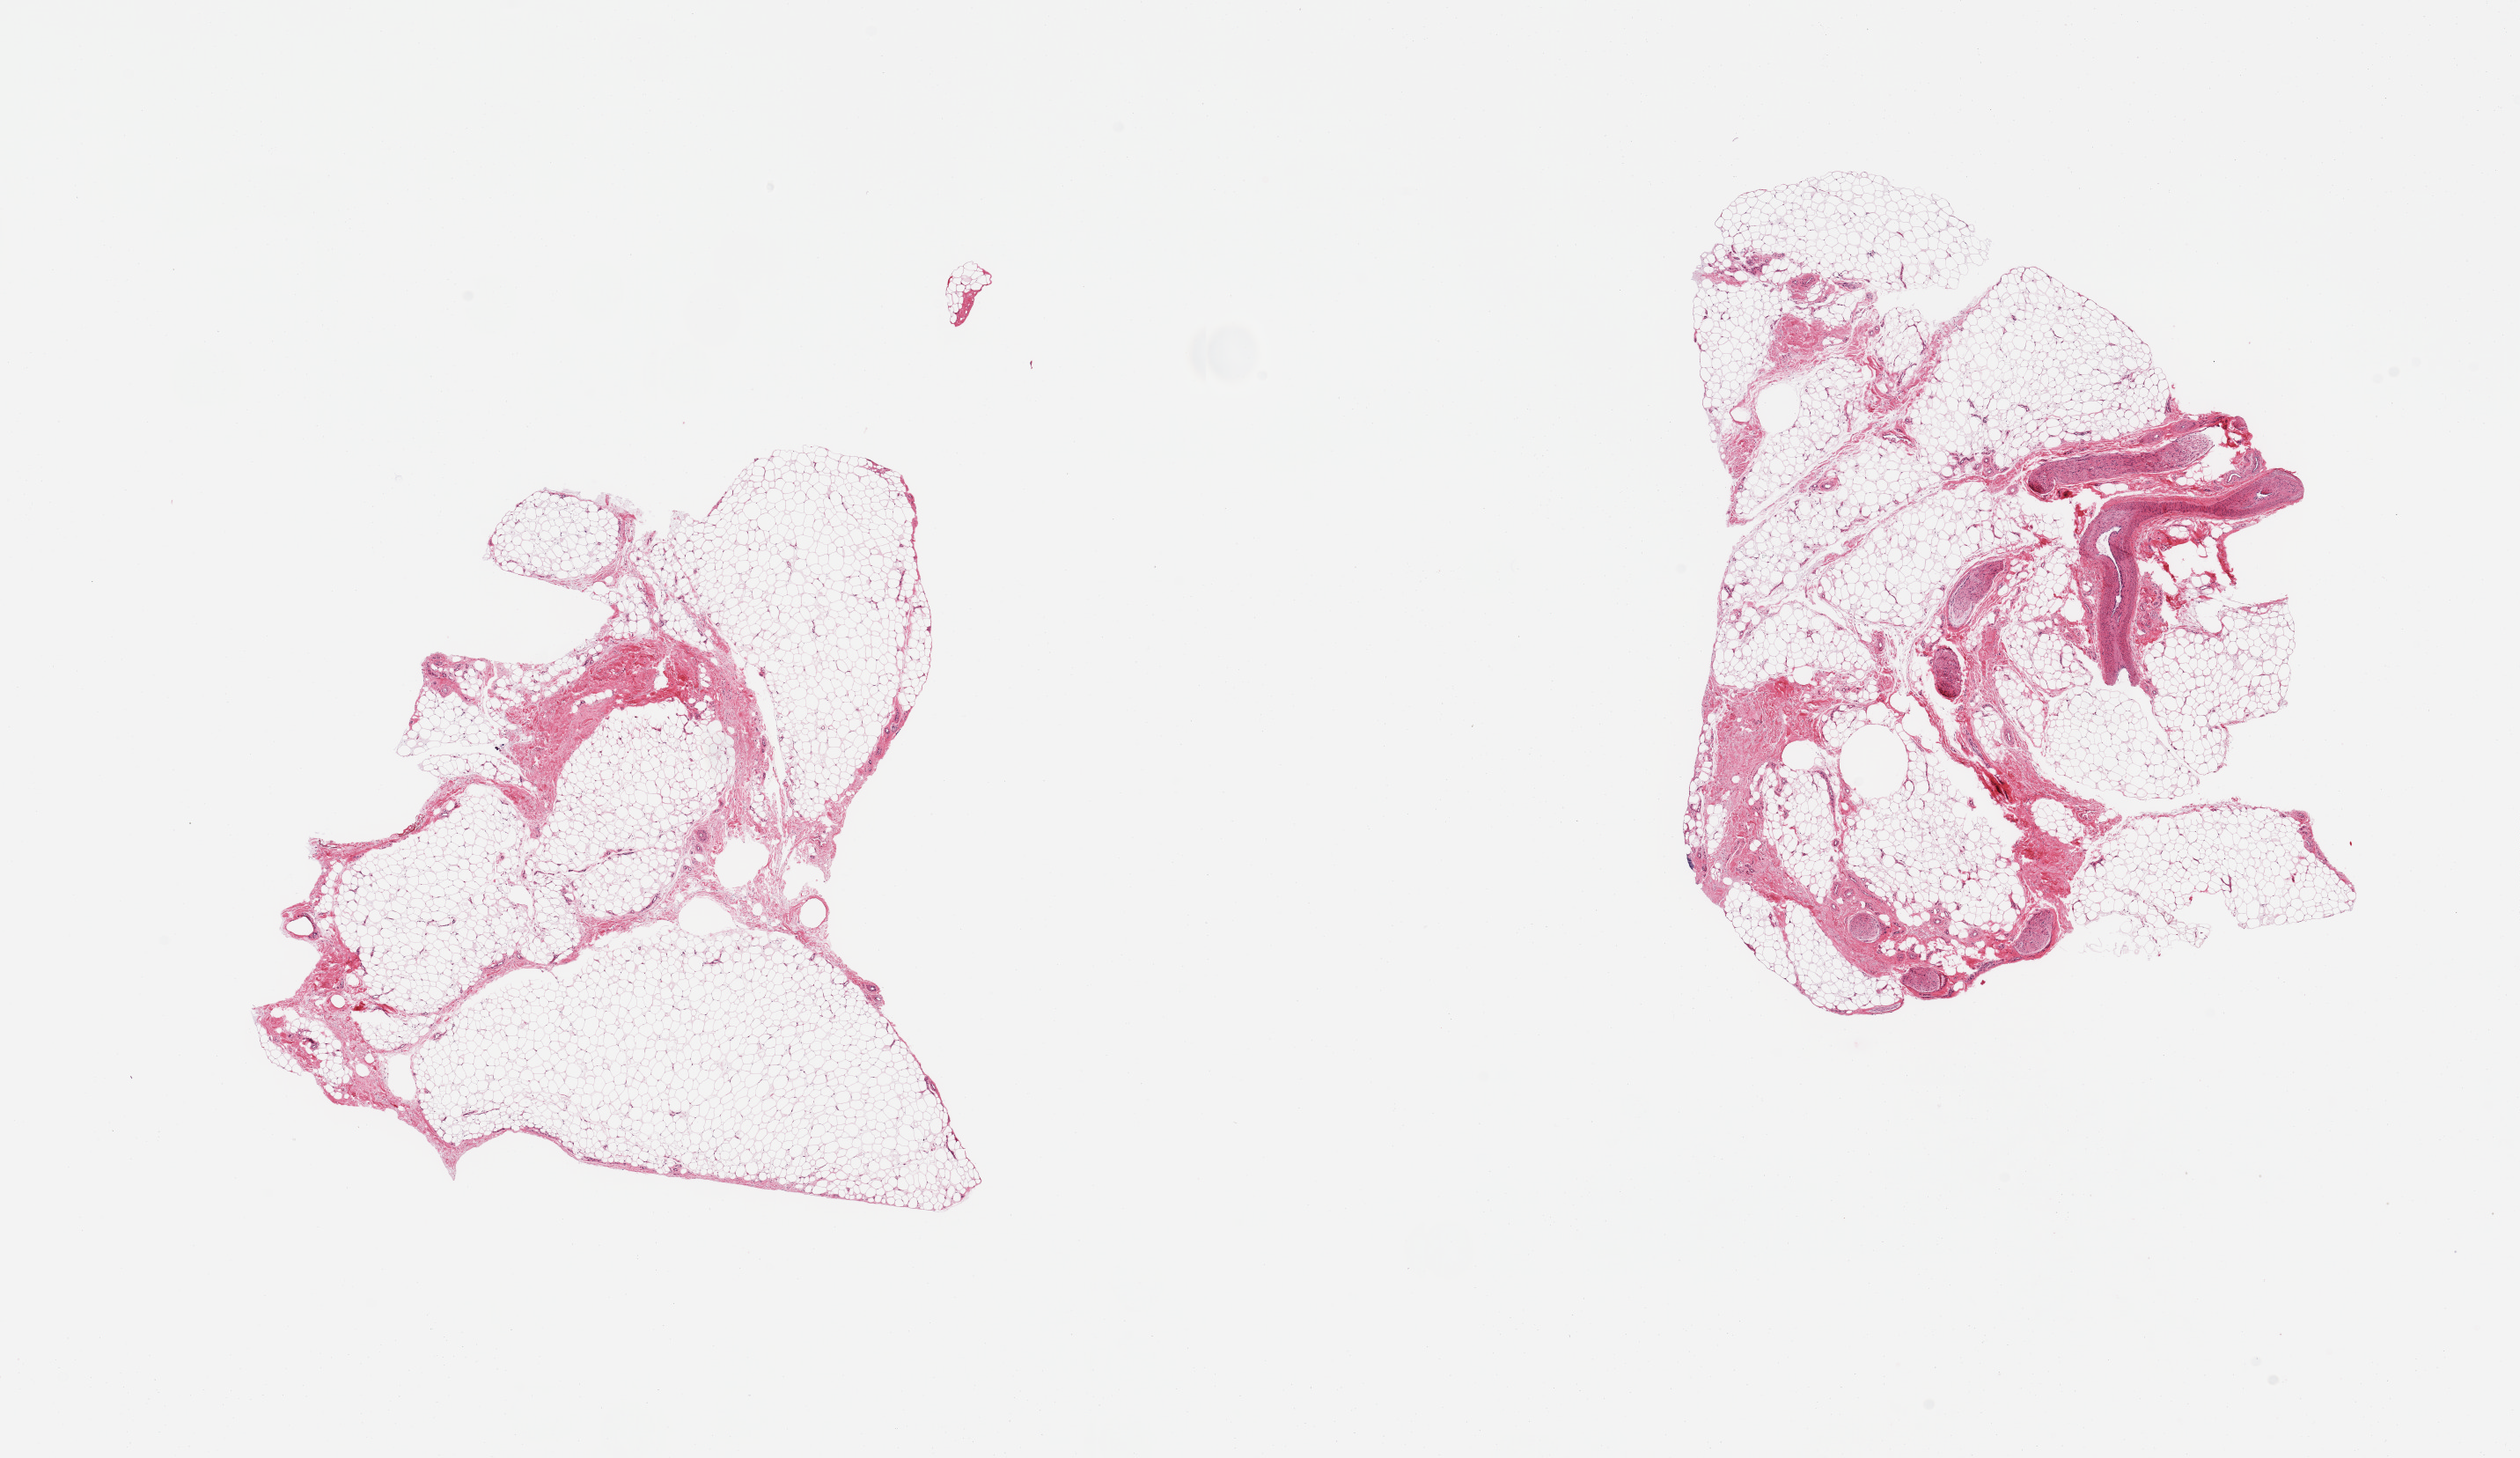
Whole-slide image, haematoxylin and eosin stain — shown as a low-resolution overview of the whole scanned area (about 22.6 x 13.1 mm); PAXgene-fixed paraffin-embedded (PFPE) section; sampled site (target tissue): adipose tissue; donor tissue sample. Male donor.
Review note (as recorded): 2 pieces; 5 & 10% fibrovascular & neural content.